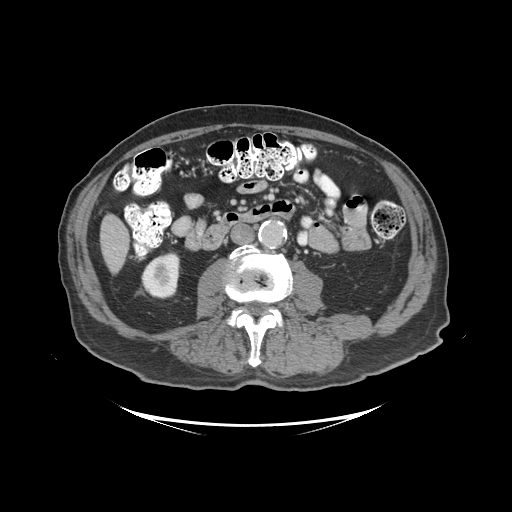
Contrast-enhanced abdominal CT (liver protocol), one axial slice. Slice 26 of 99 in the series (ordered by position). Reconstruction kernel STANDARD. Soft-tissue window (W 400 / L 40 HU). 512 × 512 image matrix. From the clinical record (not read from this slice): diagnosis: hepatocellular carcinoma (patient treated with transarterial chemoembolisation; whether this scan precedes or follows treatment is not stated here); TNM stage (as recorded): Stage-I; Child-Pugh class: A; tumour differentiation: moderately differentiated.
Outlined on this slice (semi-automatic segmentation, software-assisted and operator-edited):
- liver parenchyma outside the tumour (the mass and vessels are separate outlines, so this box may not span the whole liver): bounding box <100,214,128,274> (left, top, right, bottom; pixels)